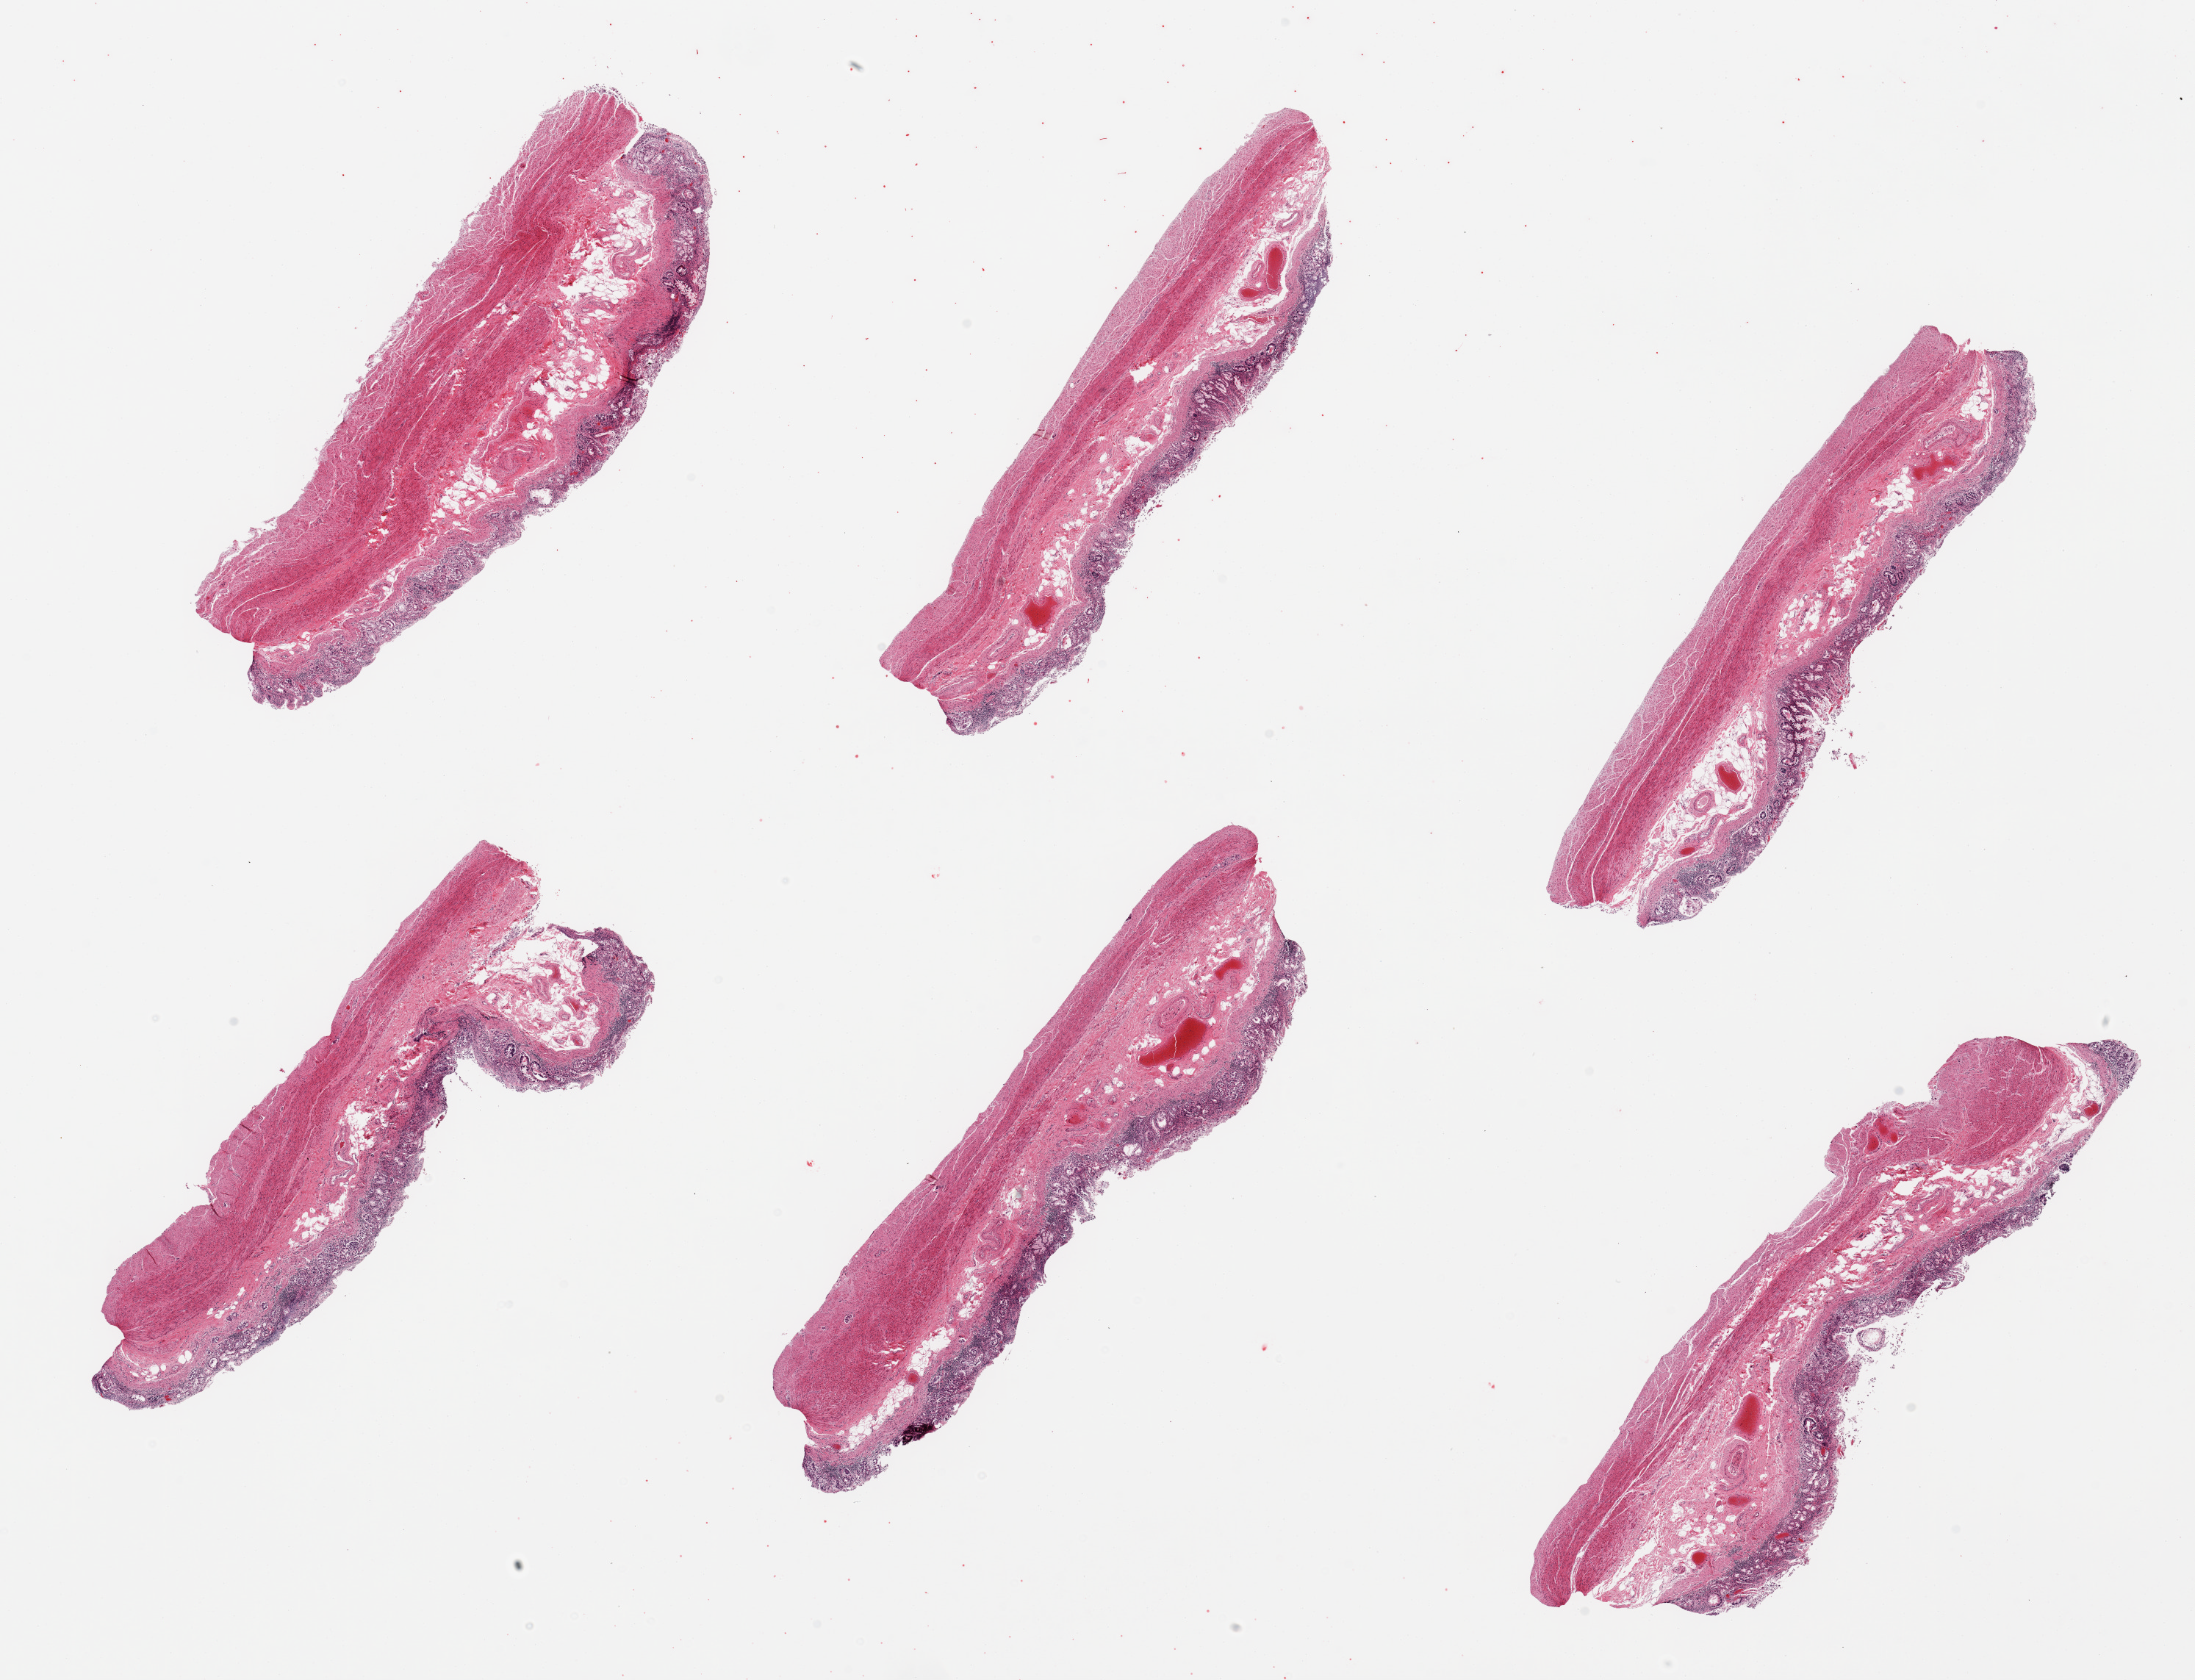
Whole-slide image, haematoxylin and eosin stain, brightfield, shown as a low-resolution overview of the whole scanned area (about 23.6 x 18.1 mm), PAXgene-fixed, paraffin-embedded tissue, section of stomach (target tissue), donor tissue sample. Donor sex: female.
Review note (as recorded): 6 pieces; marked chronic gastritis; mucosa mostly autolyzed; muscle intact.